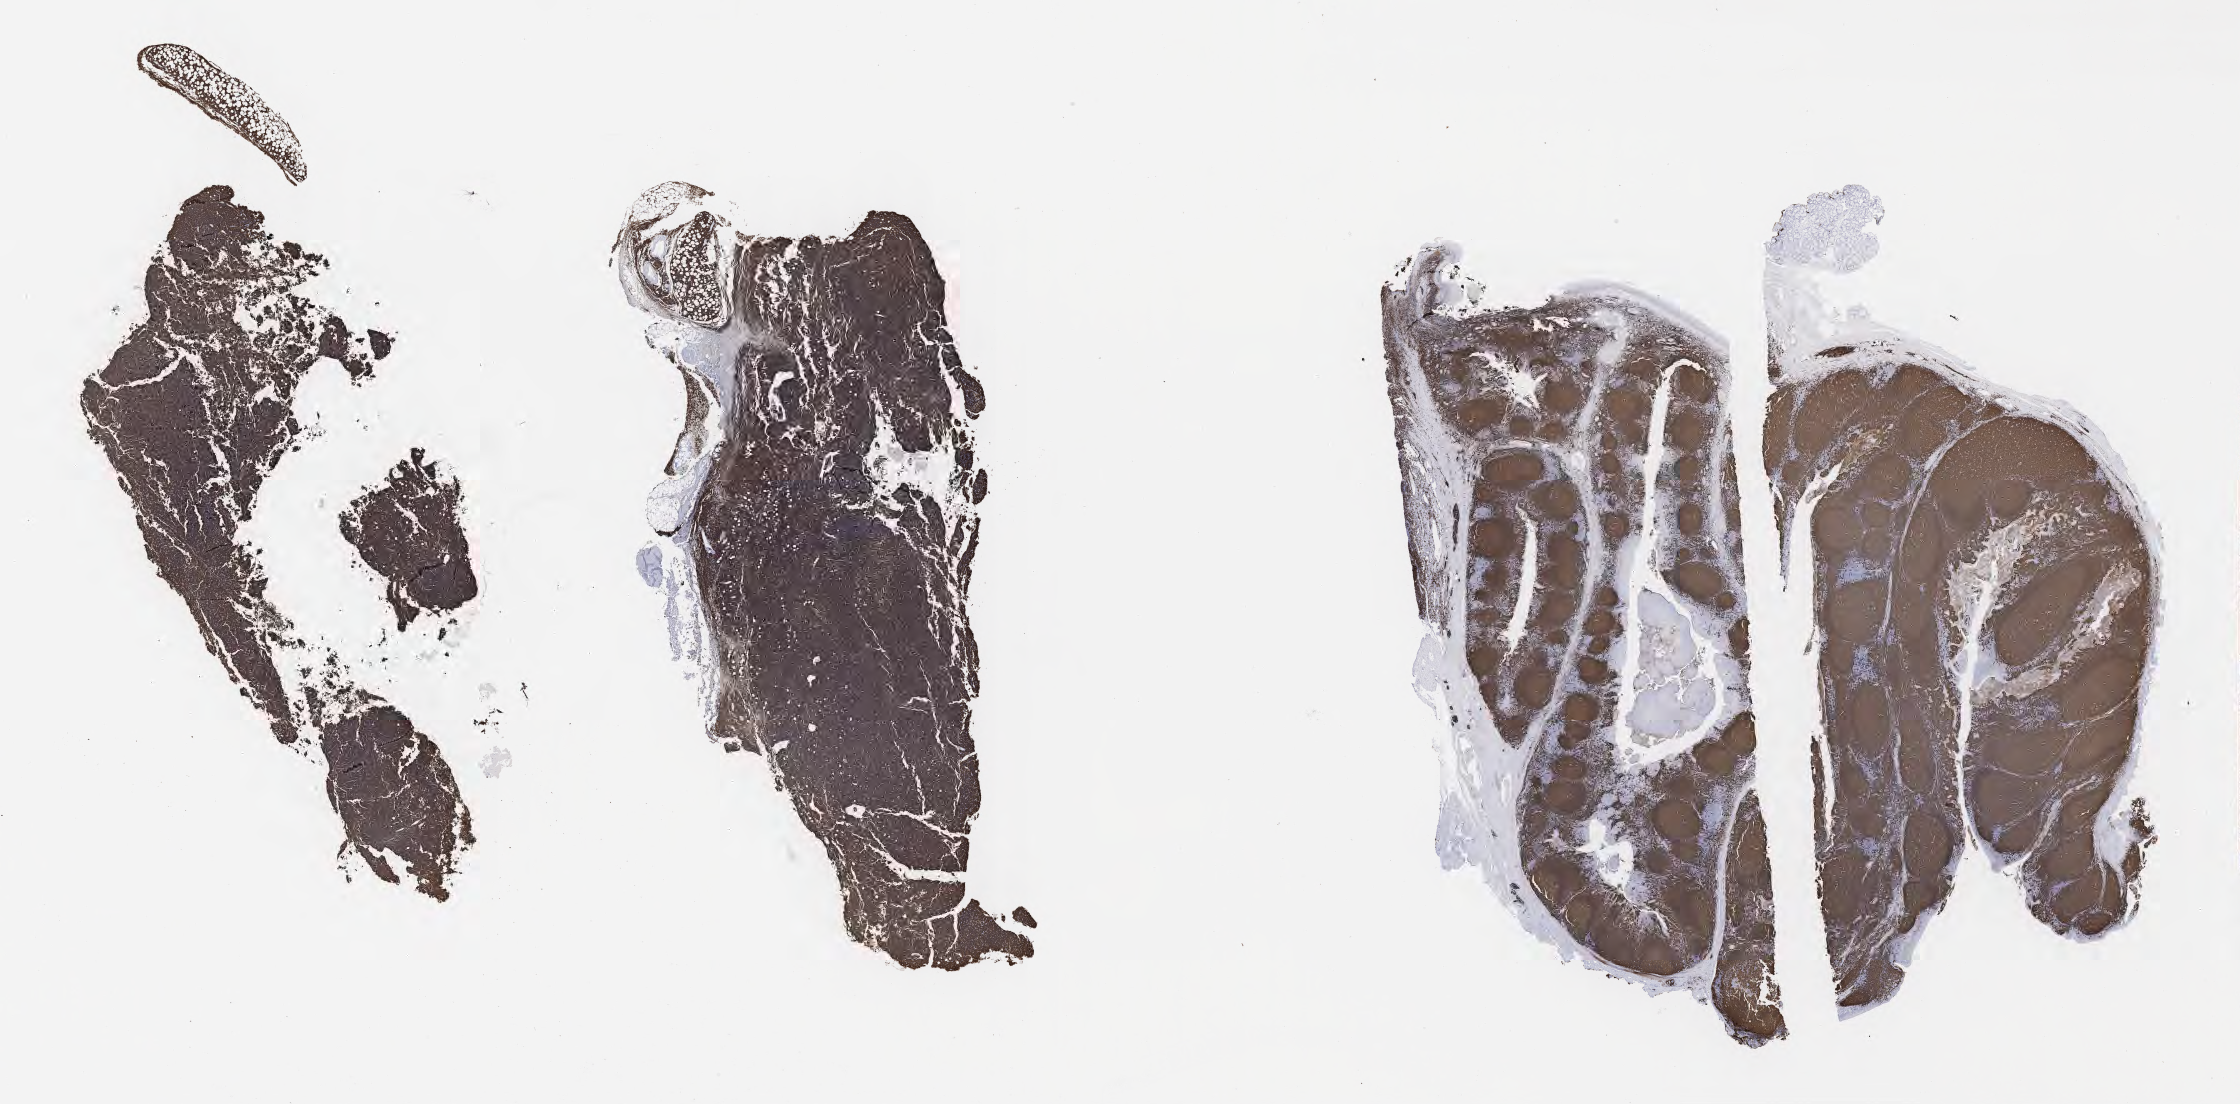
Immunohistochemistry (IHC) whole-slide image stained for CD20 — low-resolution overview of the scanned area, about 36.2 x 17.9 mm. Tumor tissue. Patient: female, age 16 years.
Diagnosis: Burkitt lymphoma, NOS.